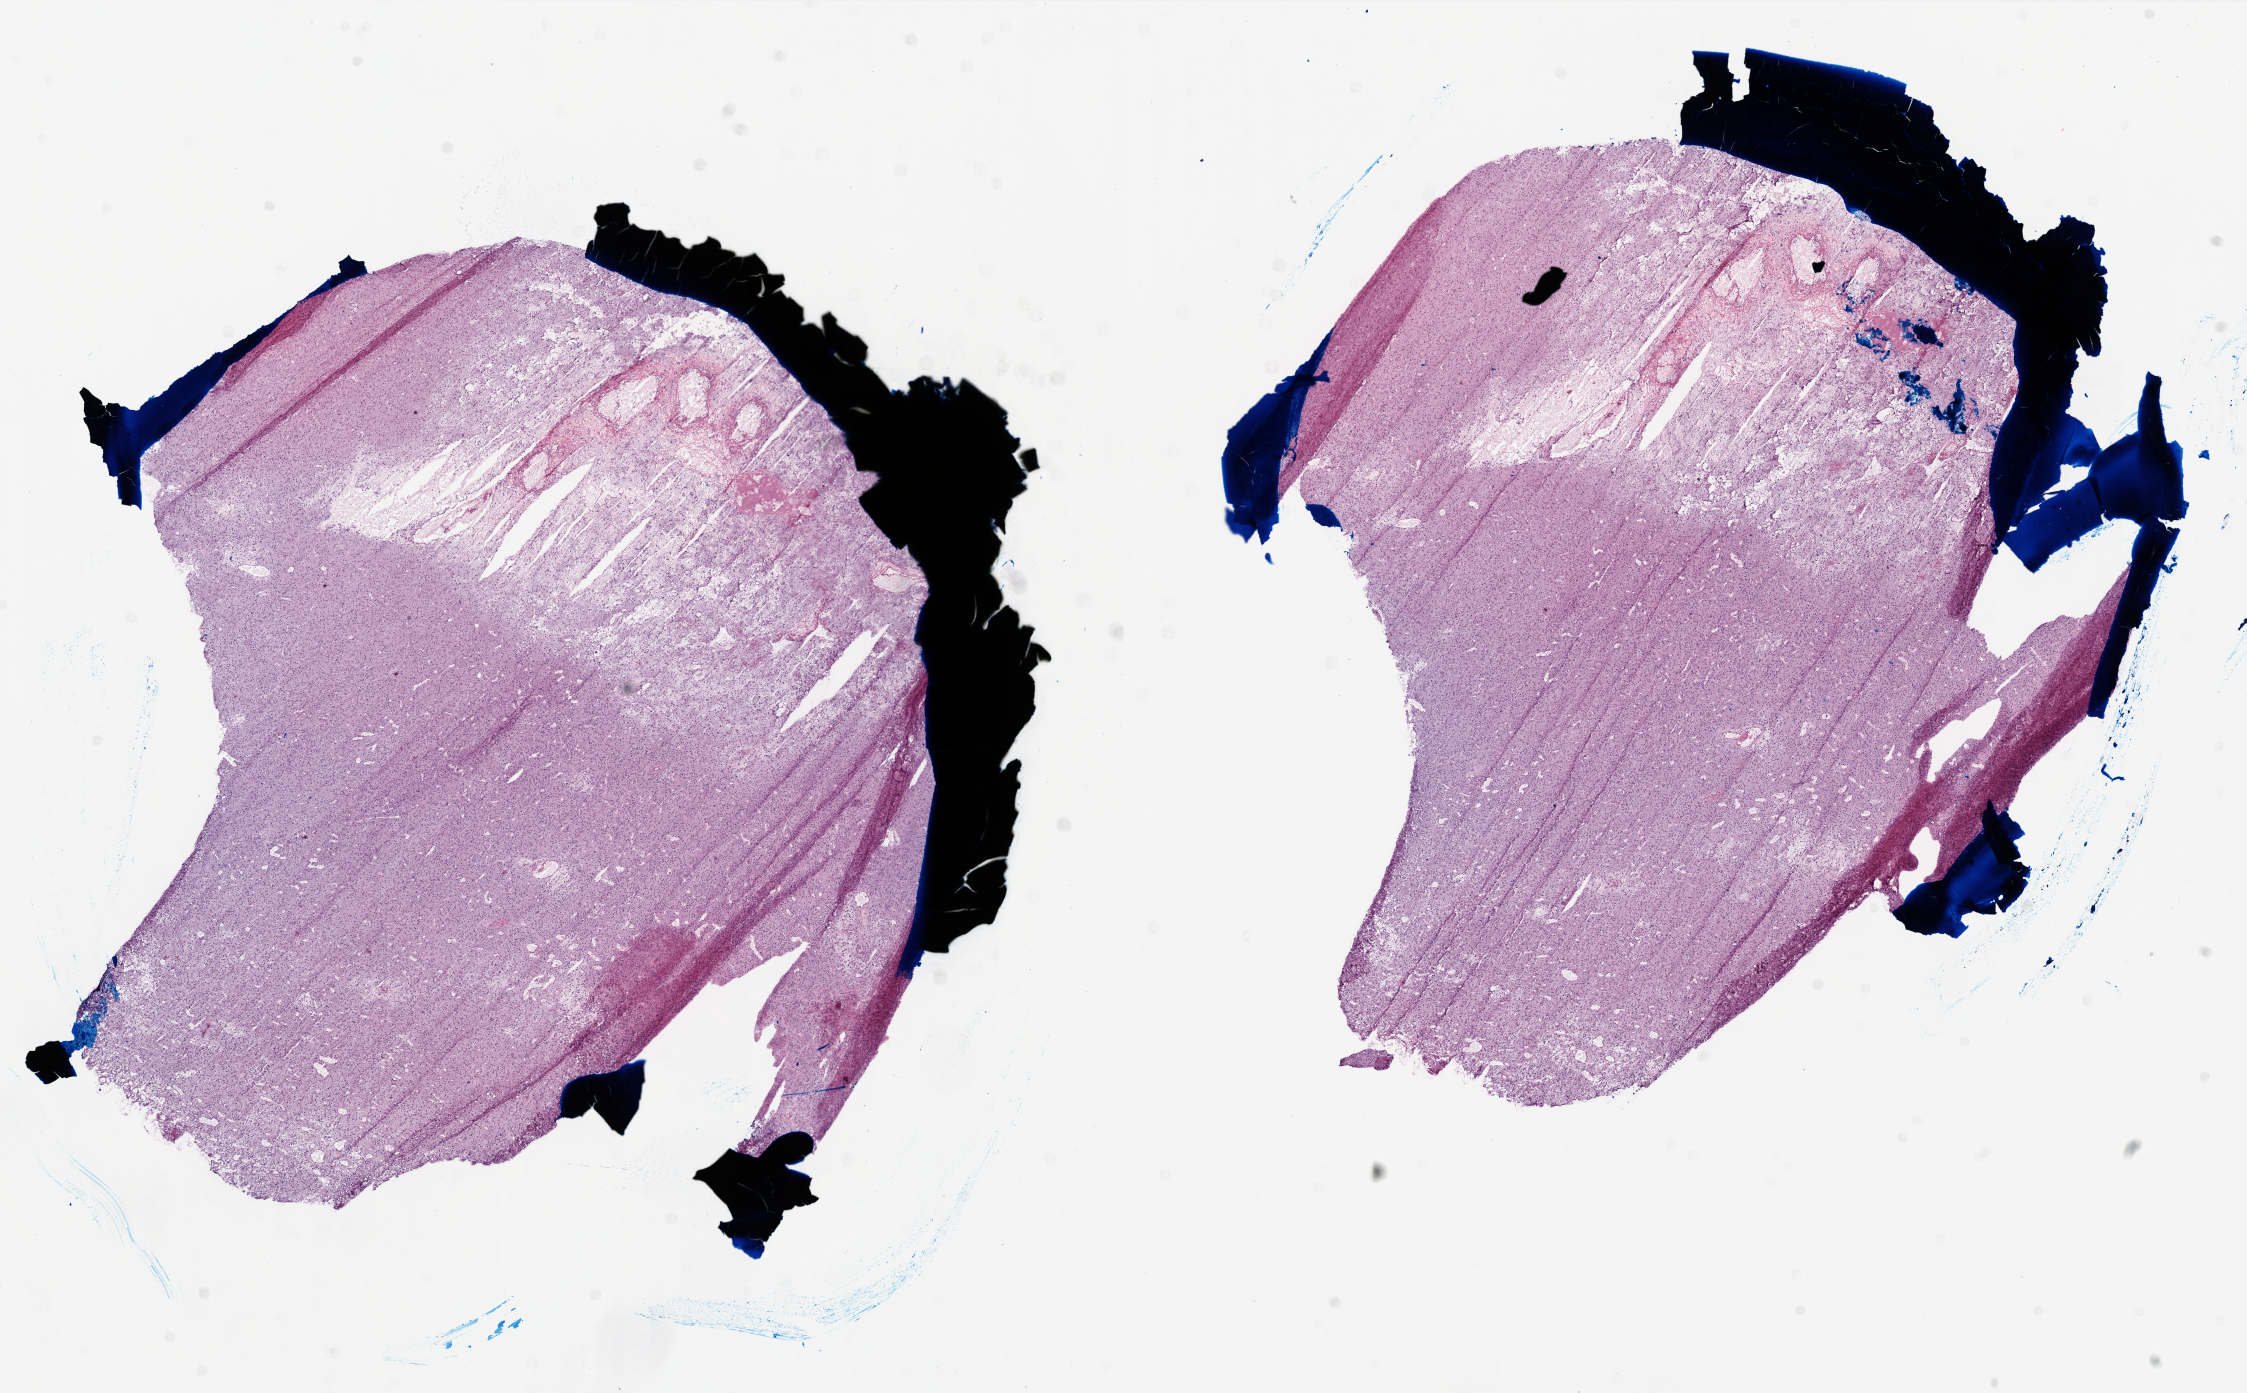
Hematoxylin and eosin (H&E) stained whole-slide image, low-resolution overview of the scanned area, about 18.0 x 11.1 mm, frozen section, sample: primary tumour, brain. Patient: female, age at initial diagnosis 52 years. Slide review estimates, as recorded: tumour cells 95%, tumour nuclei 100%.
Diagnosis: Glioblastoma.